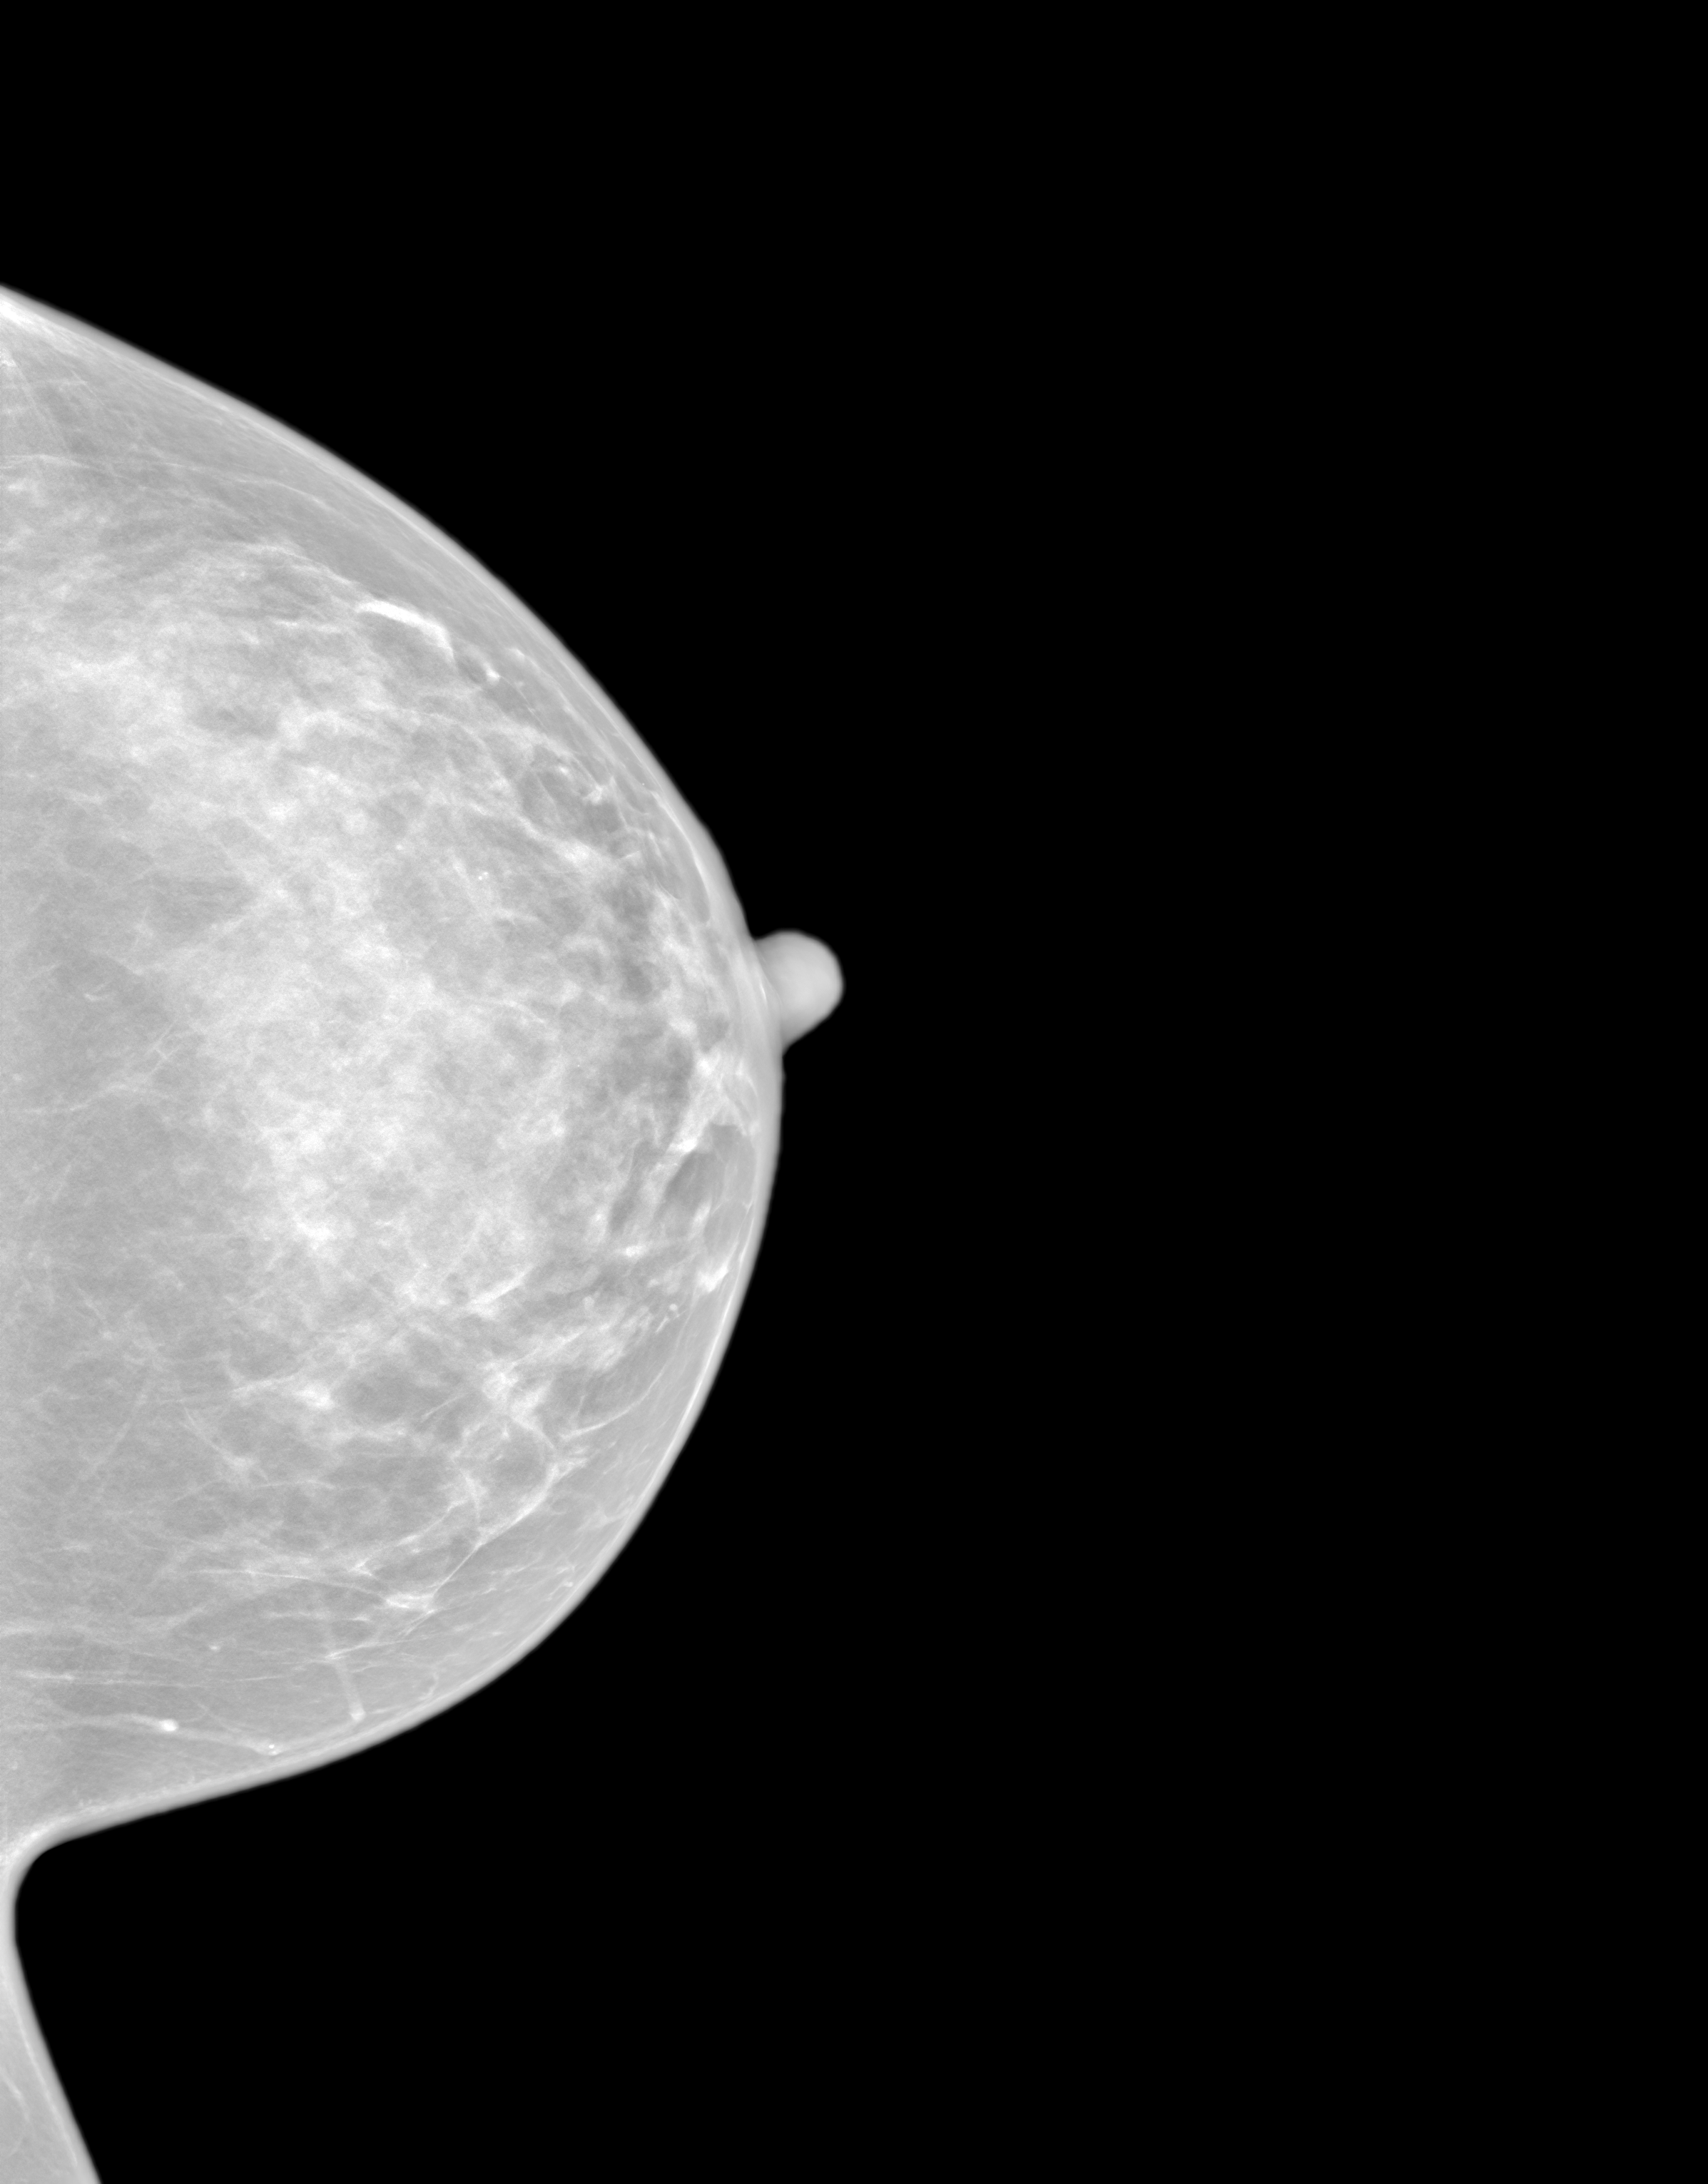
Synthetic 2-D view generated from a tomosynthesis acquisition (not an FFDM exposure); left breast; CC view; screening examination. Female patient, age 49 years.
Breast density at the screening exam (both breasts): heterogeneously dense (BI-RADS density category c). Final BI-RADS assessment for this screening round (tomosynthesis exam, both breasts): category 1. Recall: no recall after this screen.